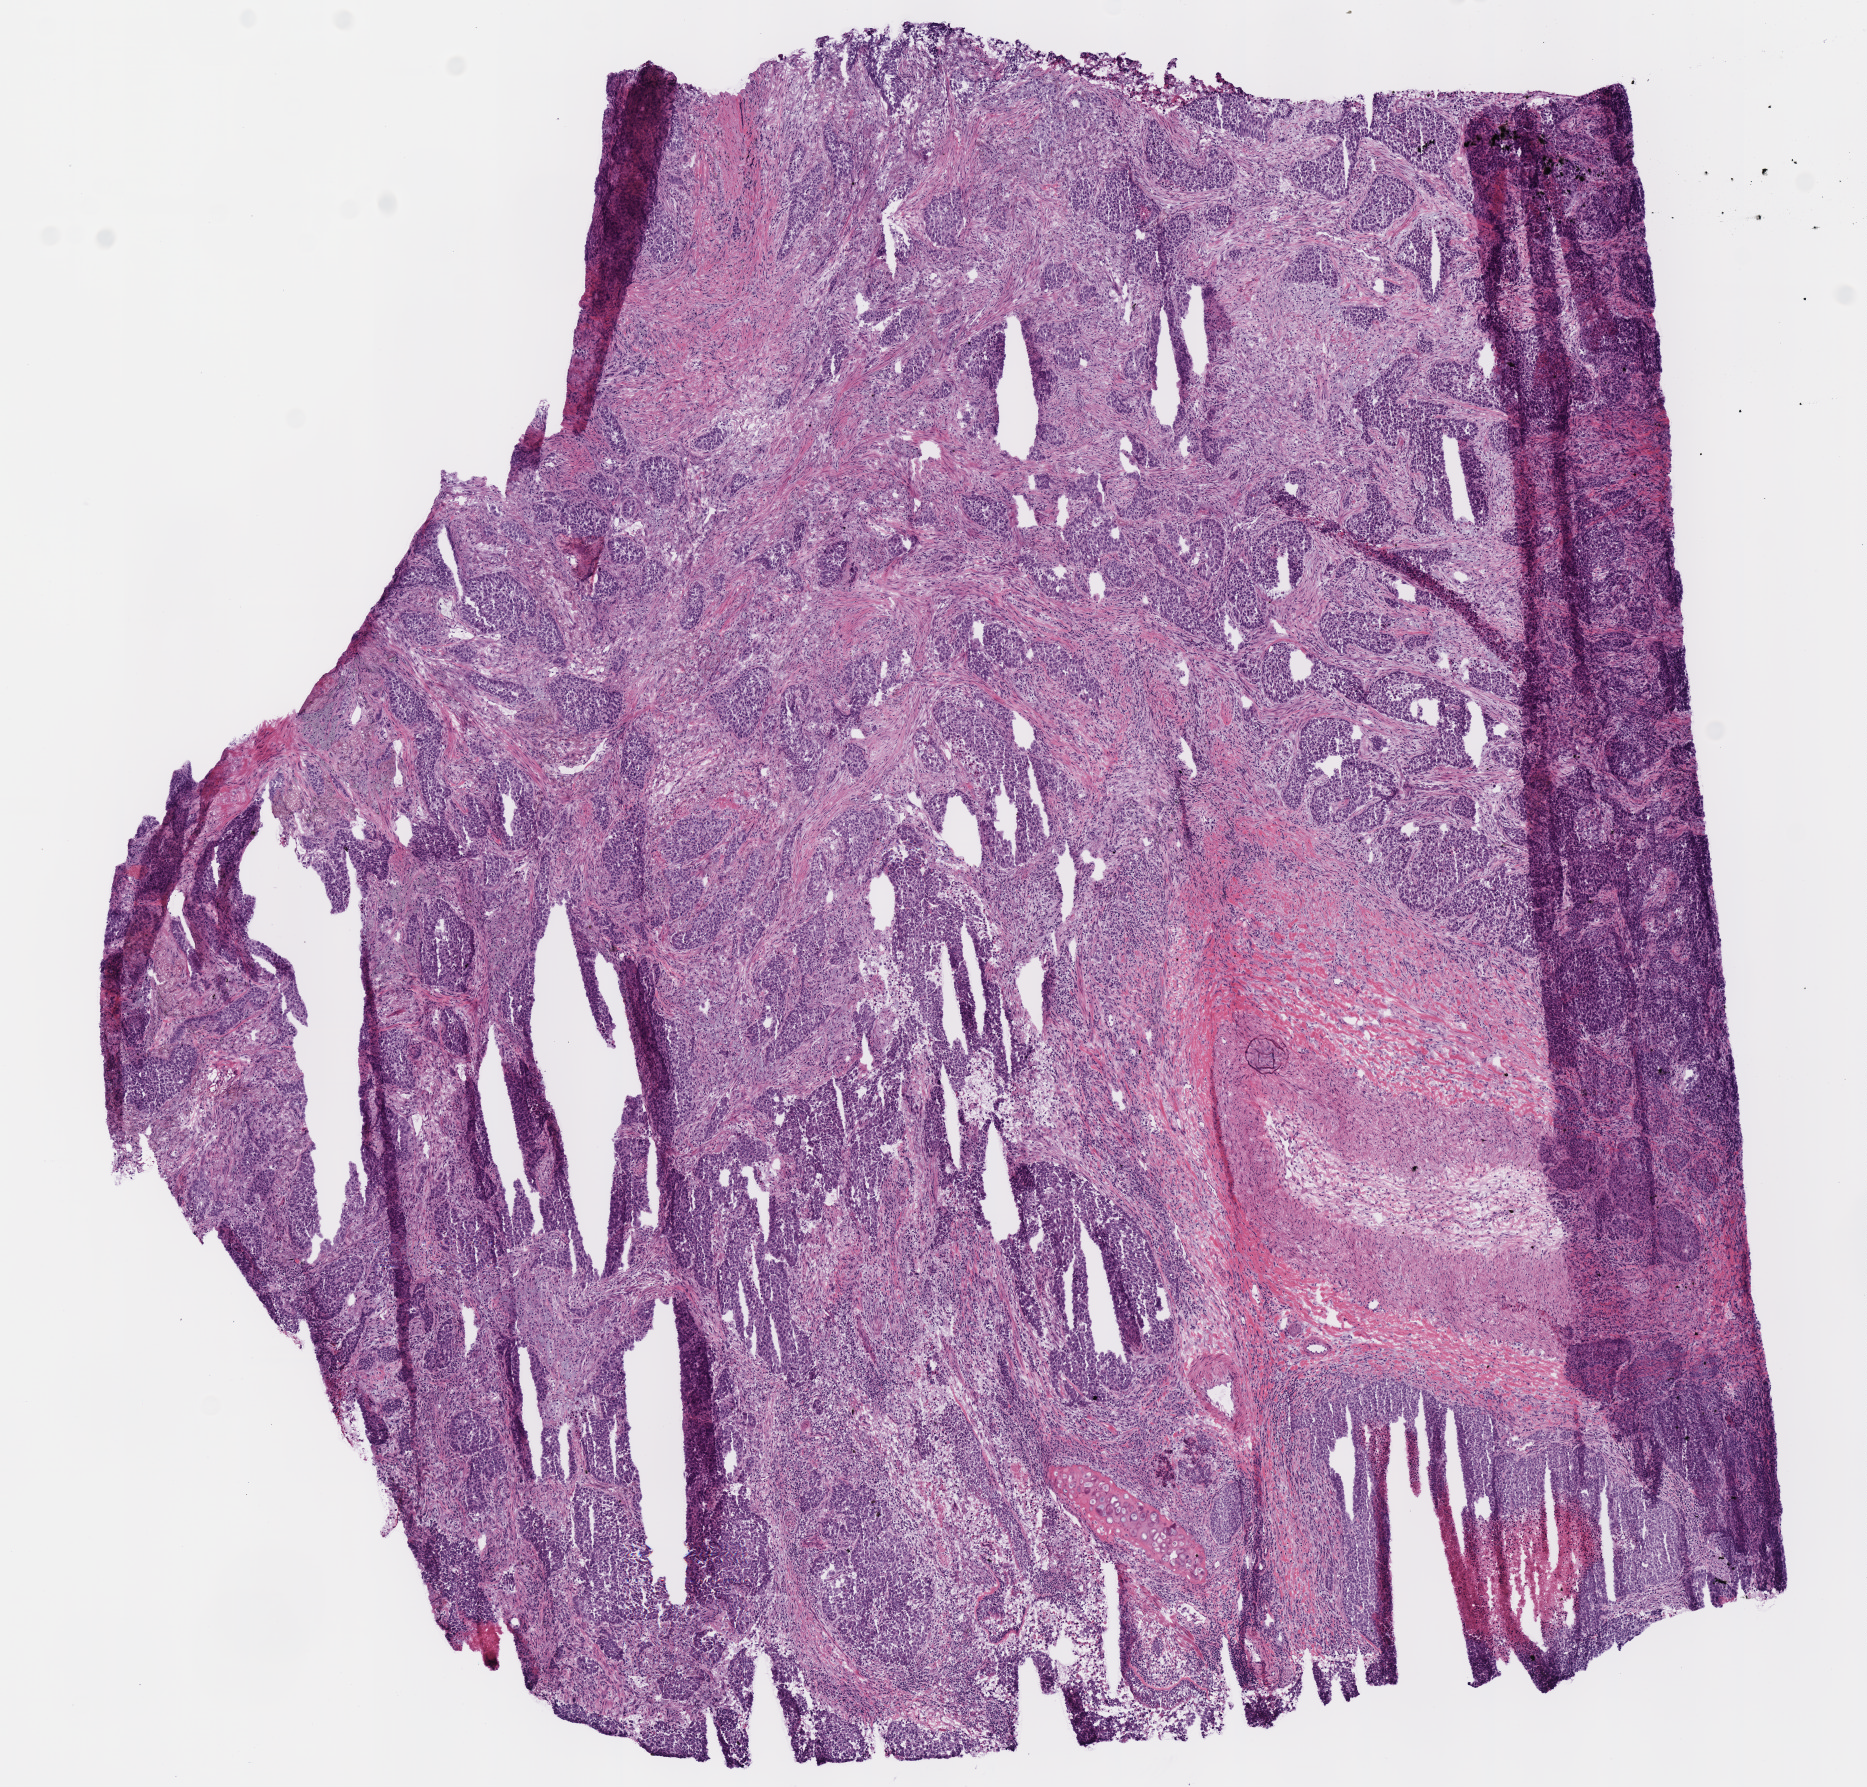
H&E-stained whole-slide image — a low-resolution overview of the entire scanned area, about 7.3 x 7.0 mm (from a 40x scan). Frozen section. Lung, primary tumour sample. Patient: male, age at initial diagnosis 72 years. Slide review estimates, as recorded: tumour cells 75%, tumour nuclei 50%, normal cells 0%, stromal cells 25%, necrosis 0%.
* AJCC pathologic stage: IB (7th edition)
* histologic diagnosis: Adenocarcinoma, NOS (upper lobe, lung)